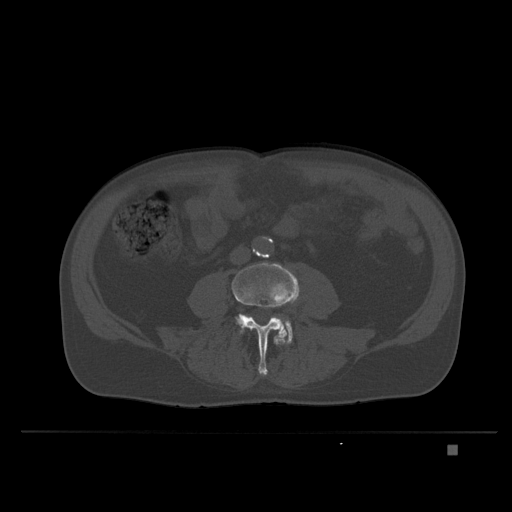
CT including the spine, one axial slice; position 73 of 435 along the scan axis; bone window (W 1800 / L 400 HU); 1.5 mm slice thickness; 512 × 512 image matrix. Patient: male, 73 years. From the clinical record (not read from this slice): primary cancer: skin.
Structures marked on this image (semi-automatic segmentation, software-assisted and operator-edited):
- L4 vertebra: bounding box [x1, y1, x2, y2] px = [232, 262, 299, 377]
- L5 vertebra: [237, 315, 292, 345]